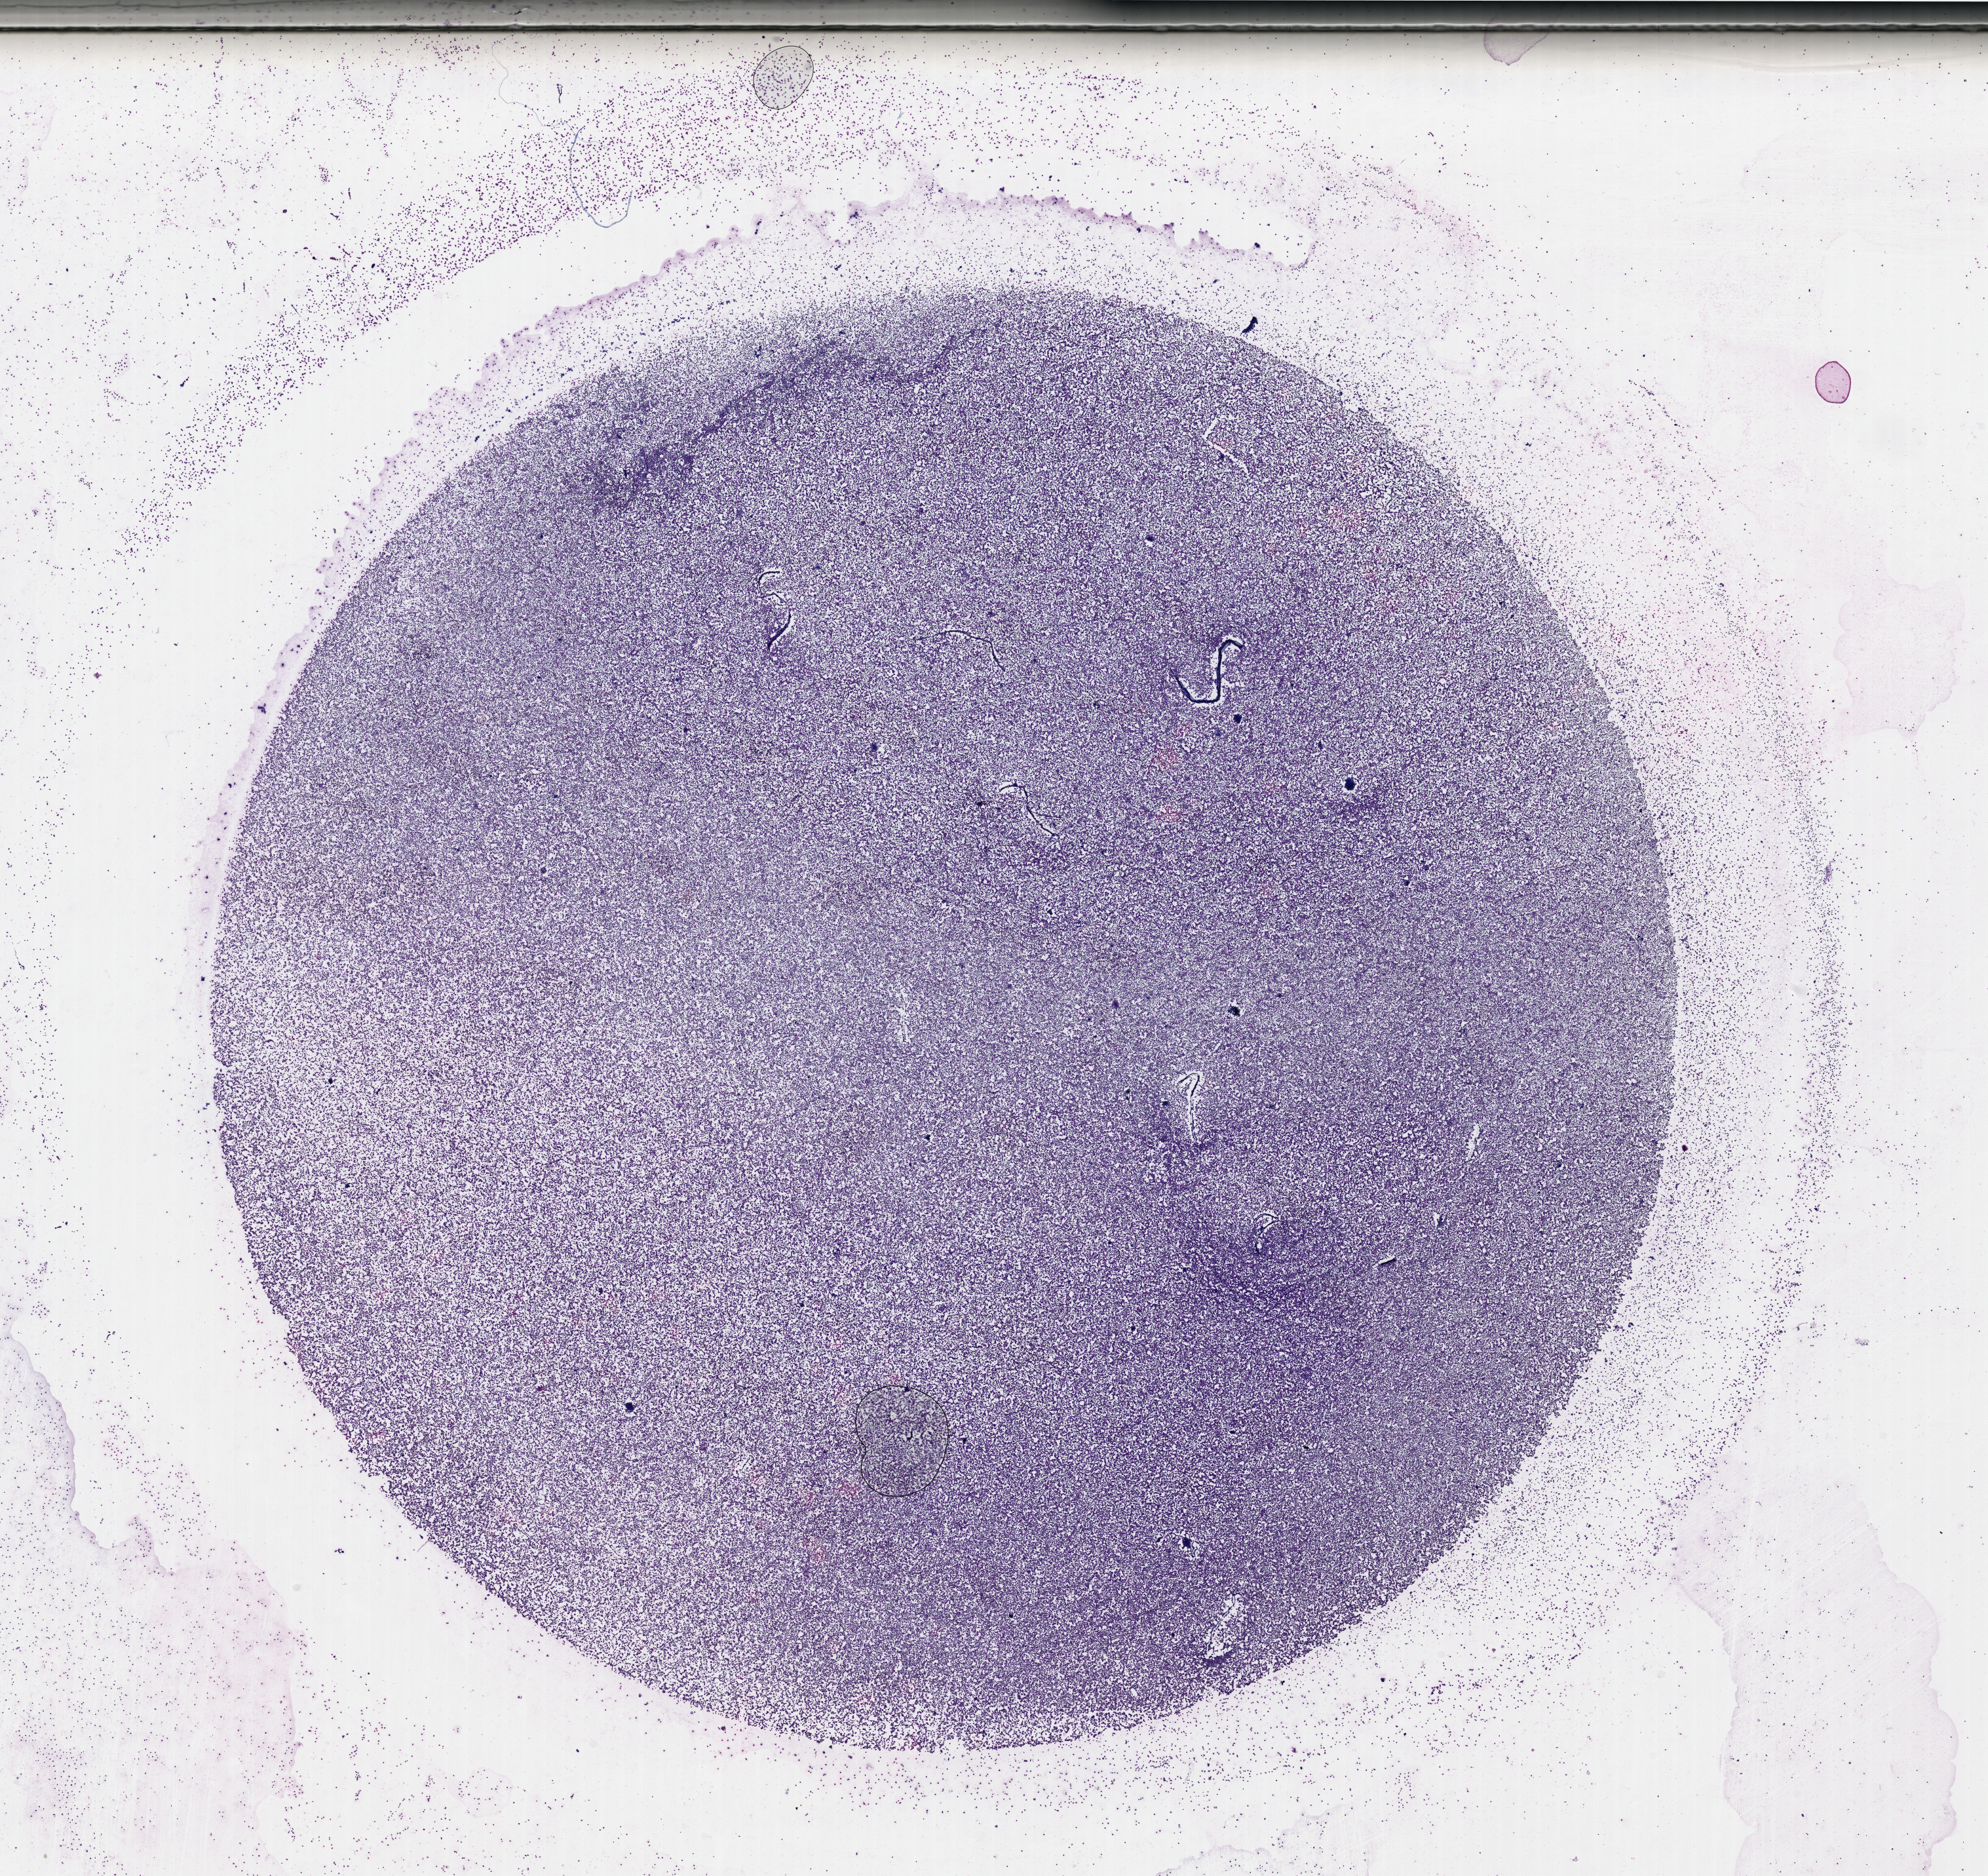
Whole-slide histology image, H&E, a low-resolution overview of the entire scanned area, about 24.0 x 22.6 mm (slide scanned at 40x); bone marrow (leukaemic) sample. 61-year-old female patient. Blasts: 80%.
FAB classification: M4. Diagnosis: Acute Myeloid Leukemia. WHO classification: Acute myelomonocytic leukemia.